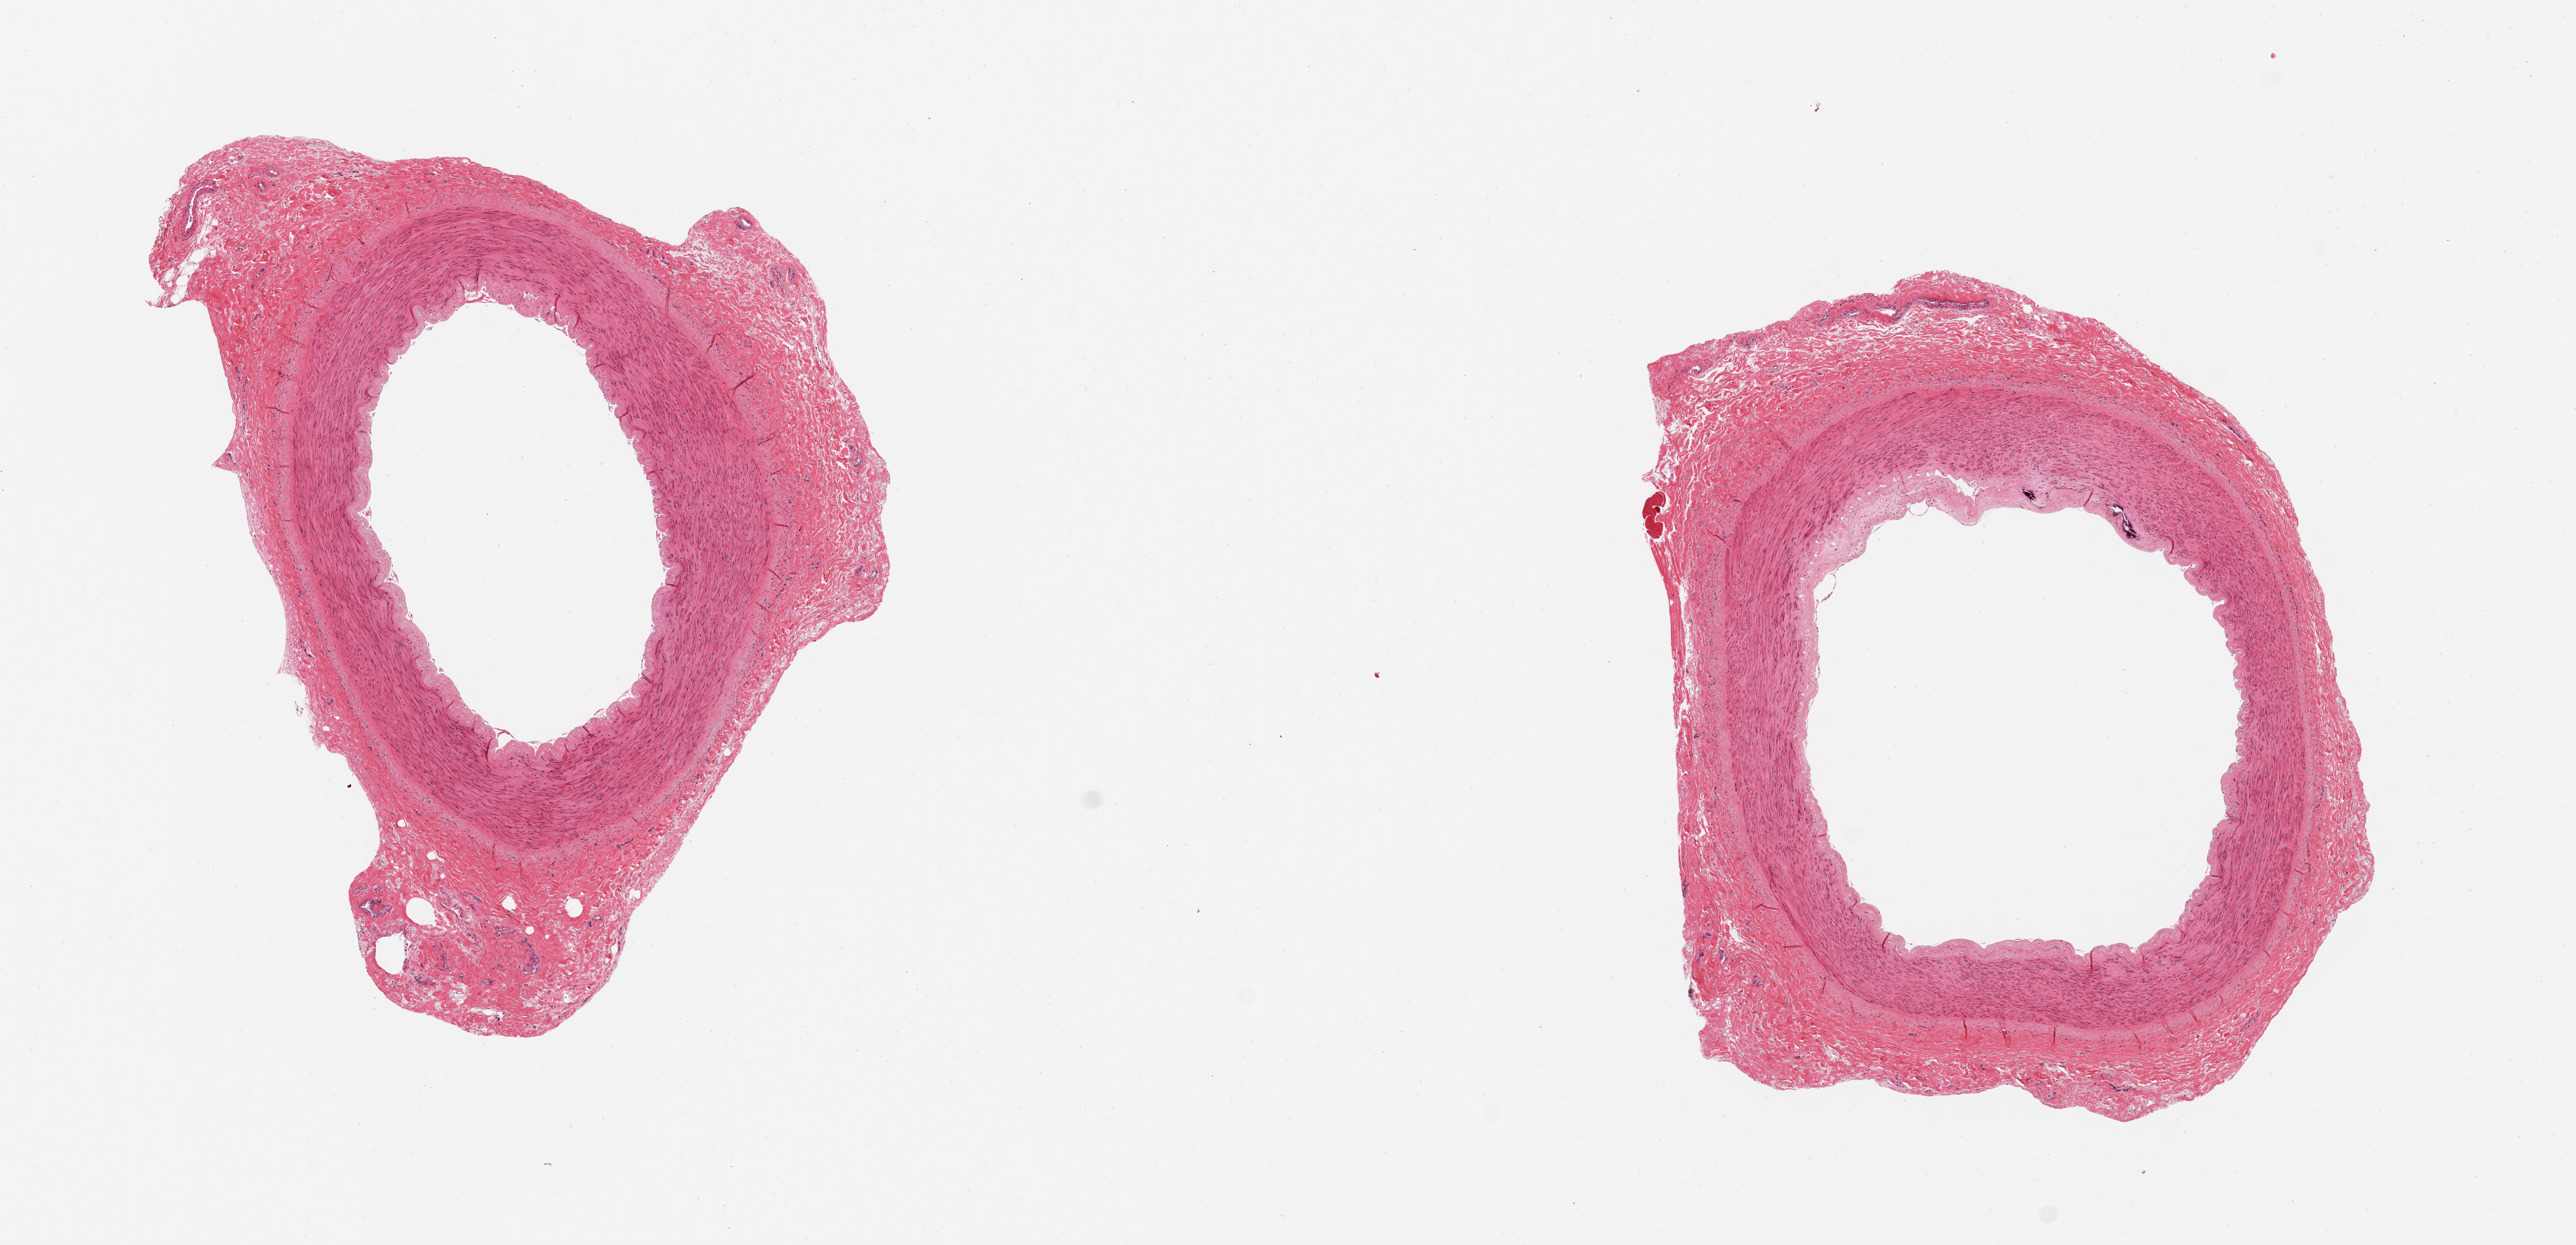
Digitized H&E-stained section — a low-resolution overview of the entire scanned area, about 14.8 x 7.1 mm (from a 20x scan); PAXgene-fixed paraffin-embedded (PFPE) section; target tissue: tibial artery; donor tissue sample. Donor sex: female.
Reviewer comment on this tissue sample: 2 pieces; minimal atherosclerosis, calcification.